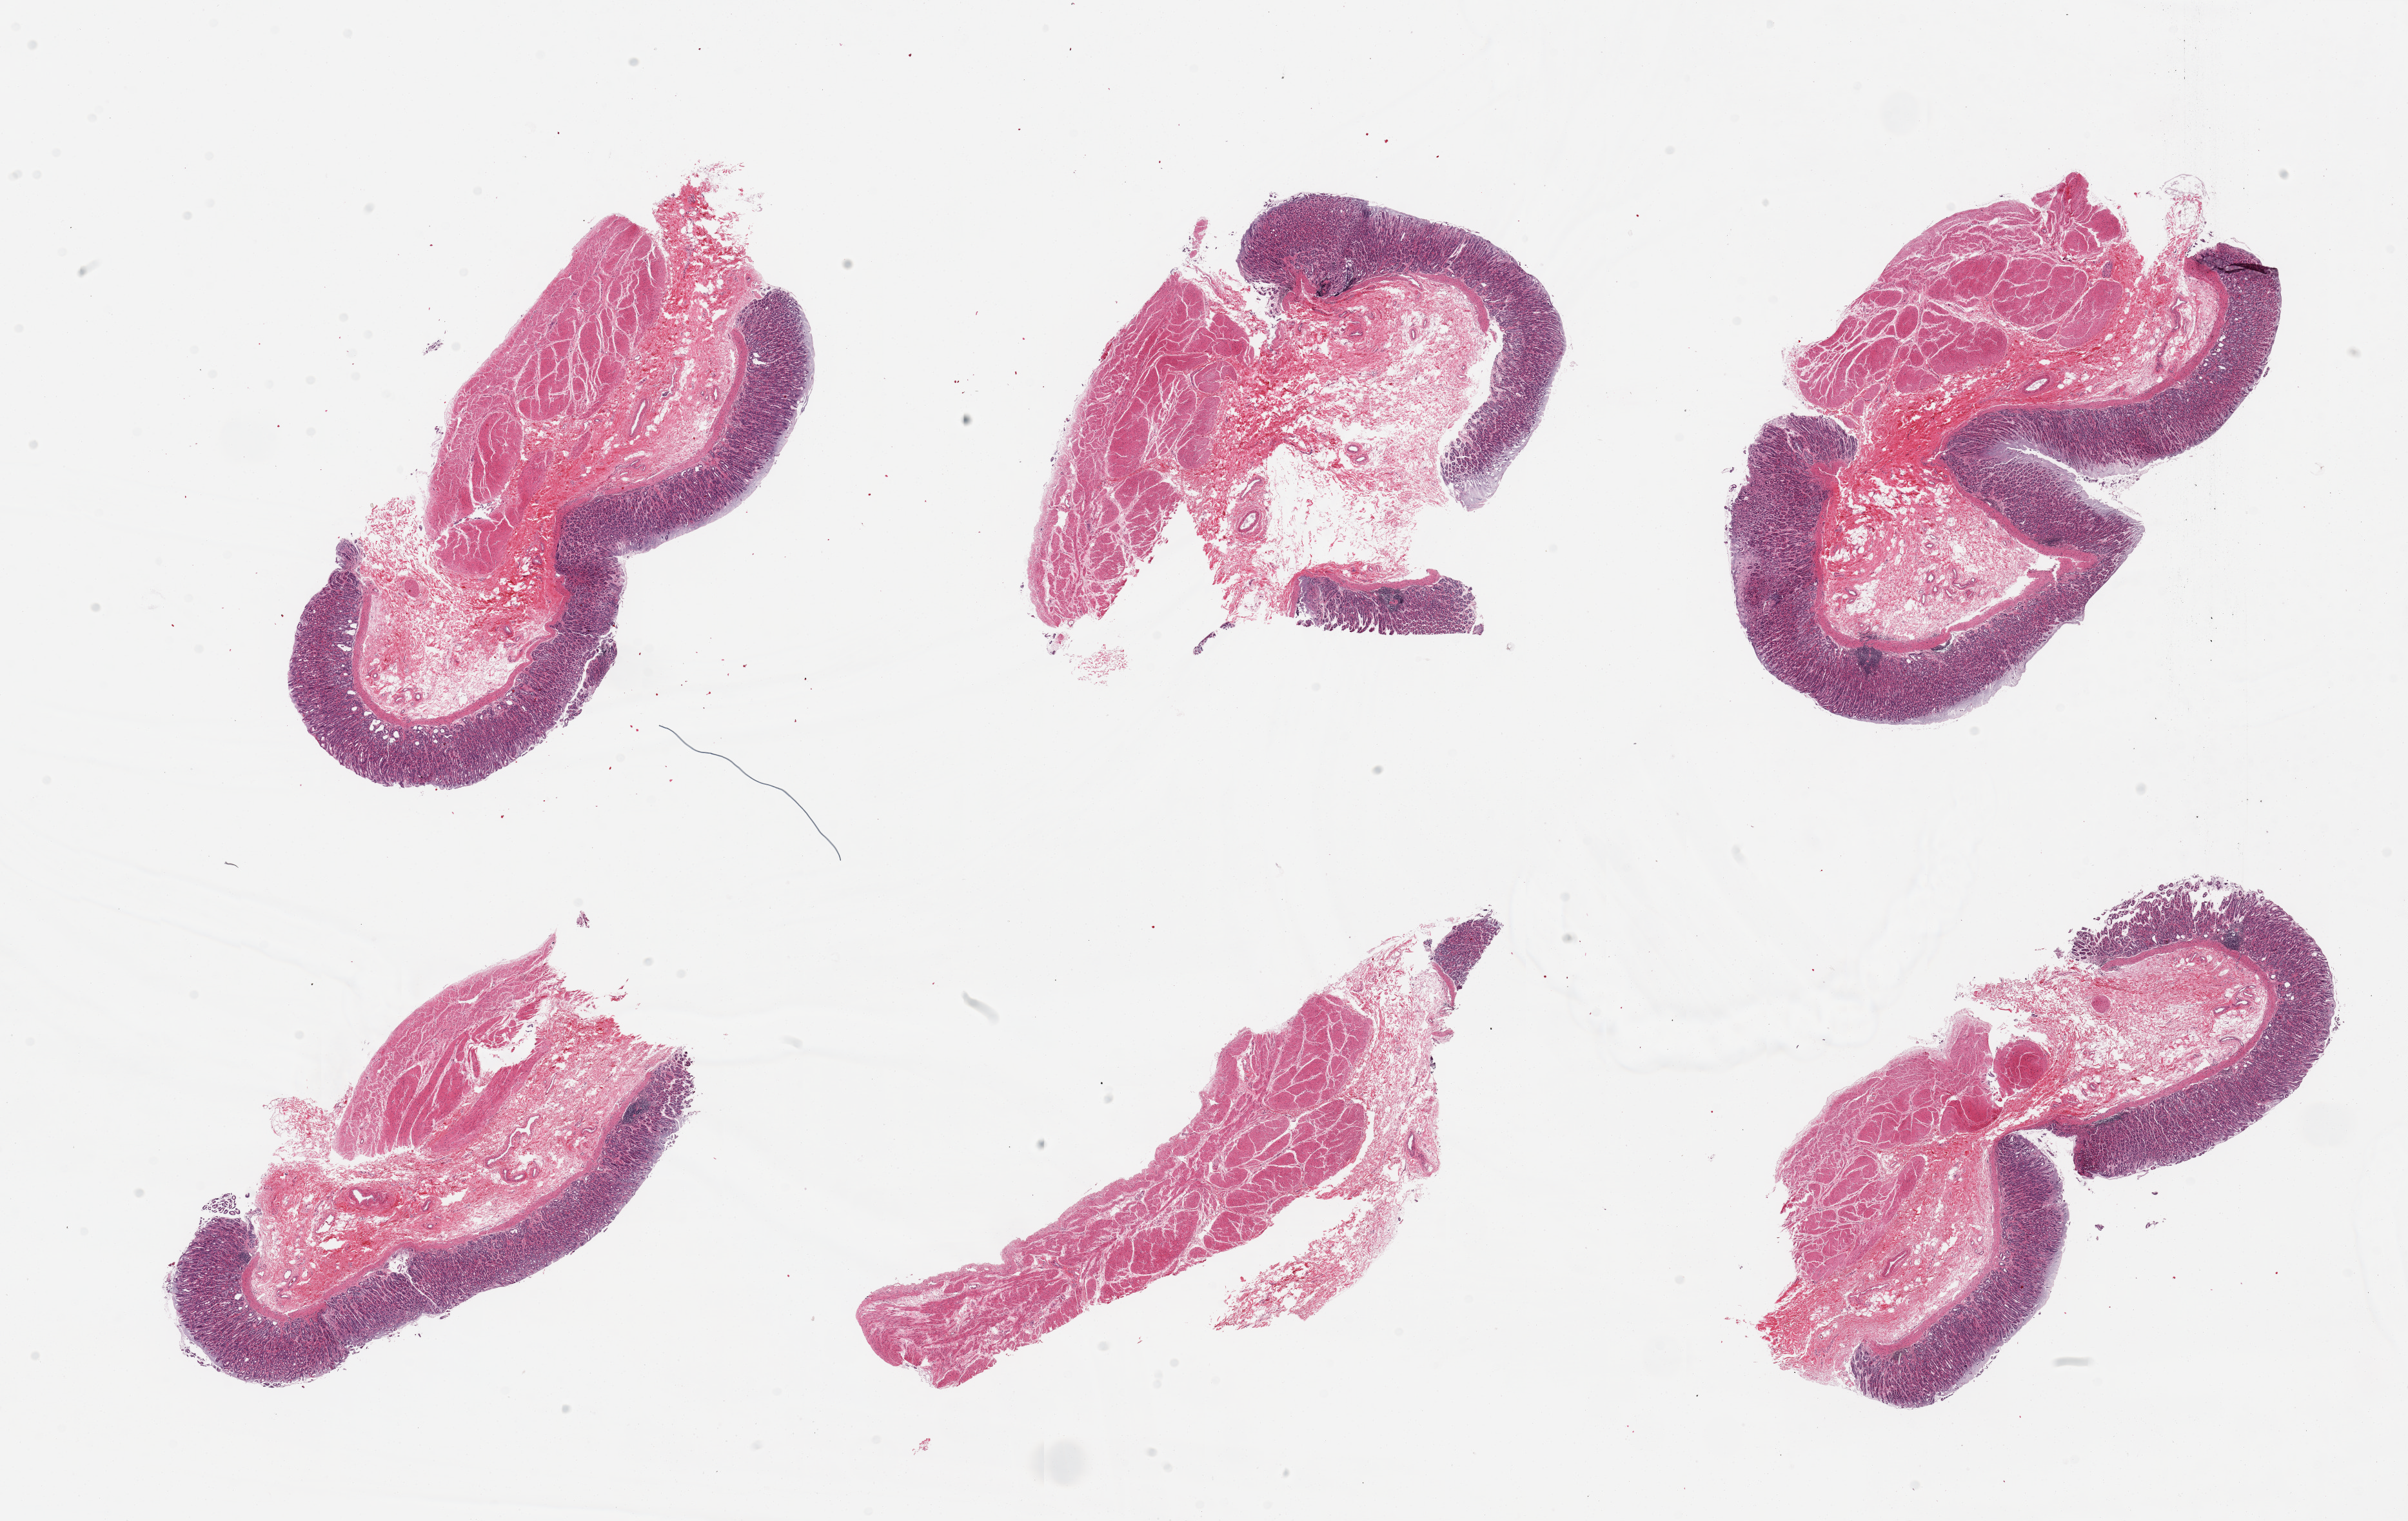
Digitized hematoxylin and eosin (H&E)-stained section, a low-resolution overview of the entire scanned area, about 29.5 x 18.7 mm (slide scanned at 20x), PAXgene-fixed, paraffin-embedded tissue, sampled site (target tissue): stomach, tissue donor sample. Donor: female.
* reviewer comment on this tissue sample: 6 pieces; all pieces include mucosa and muscularis, generally well preserved mucosa except for superficial glands